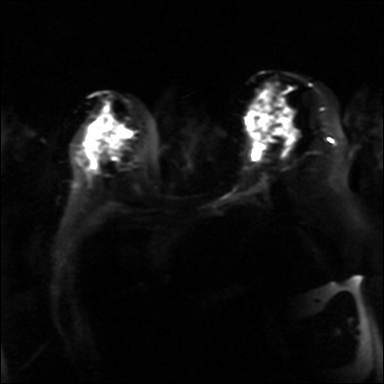
Breast MRI, one axial slice; slice 19 of 36 in the series (ordered by position); diffusion-weighted series; image 2 of 4 stored at this slice position (different b-values; order by instance number); 3 T; 4 mm slice thickness; 384 × 384 image matrix, field of view 320 × 320 mm. Female patient.
Annotated regions visible in this slice (expert manual segmentation):
- tumour on diffusion-weighted imaging: bounding box <276,128,282,132> (left, top, right, bottom; pixels)